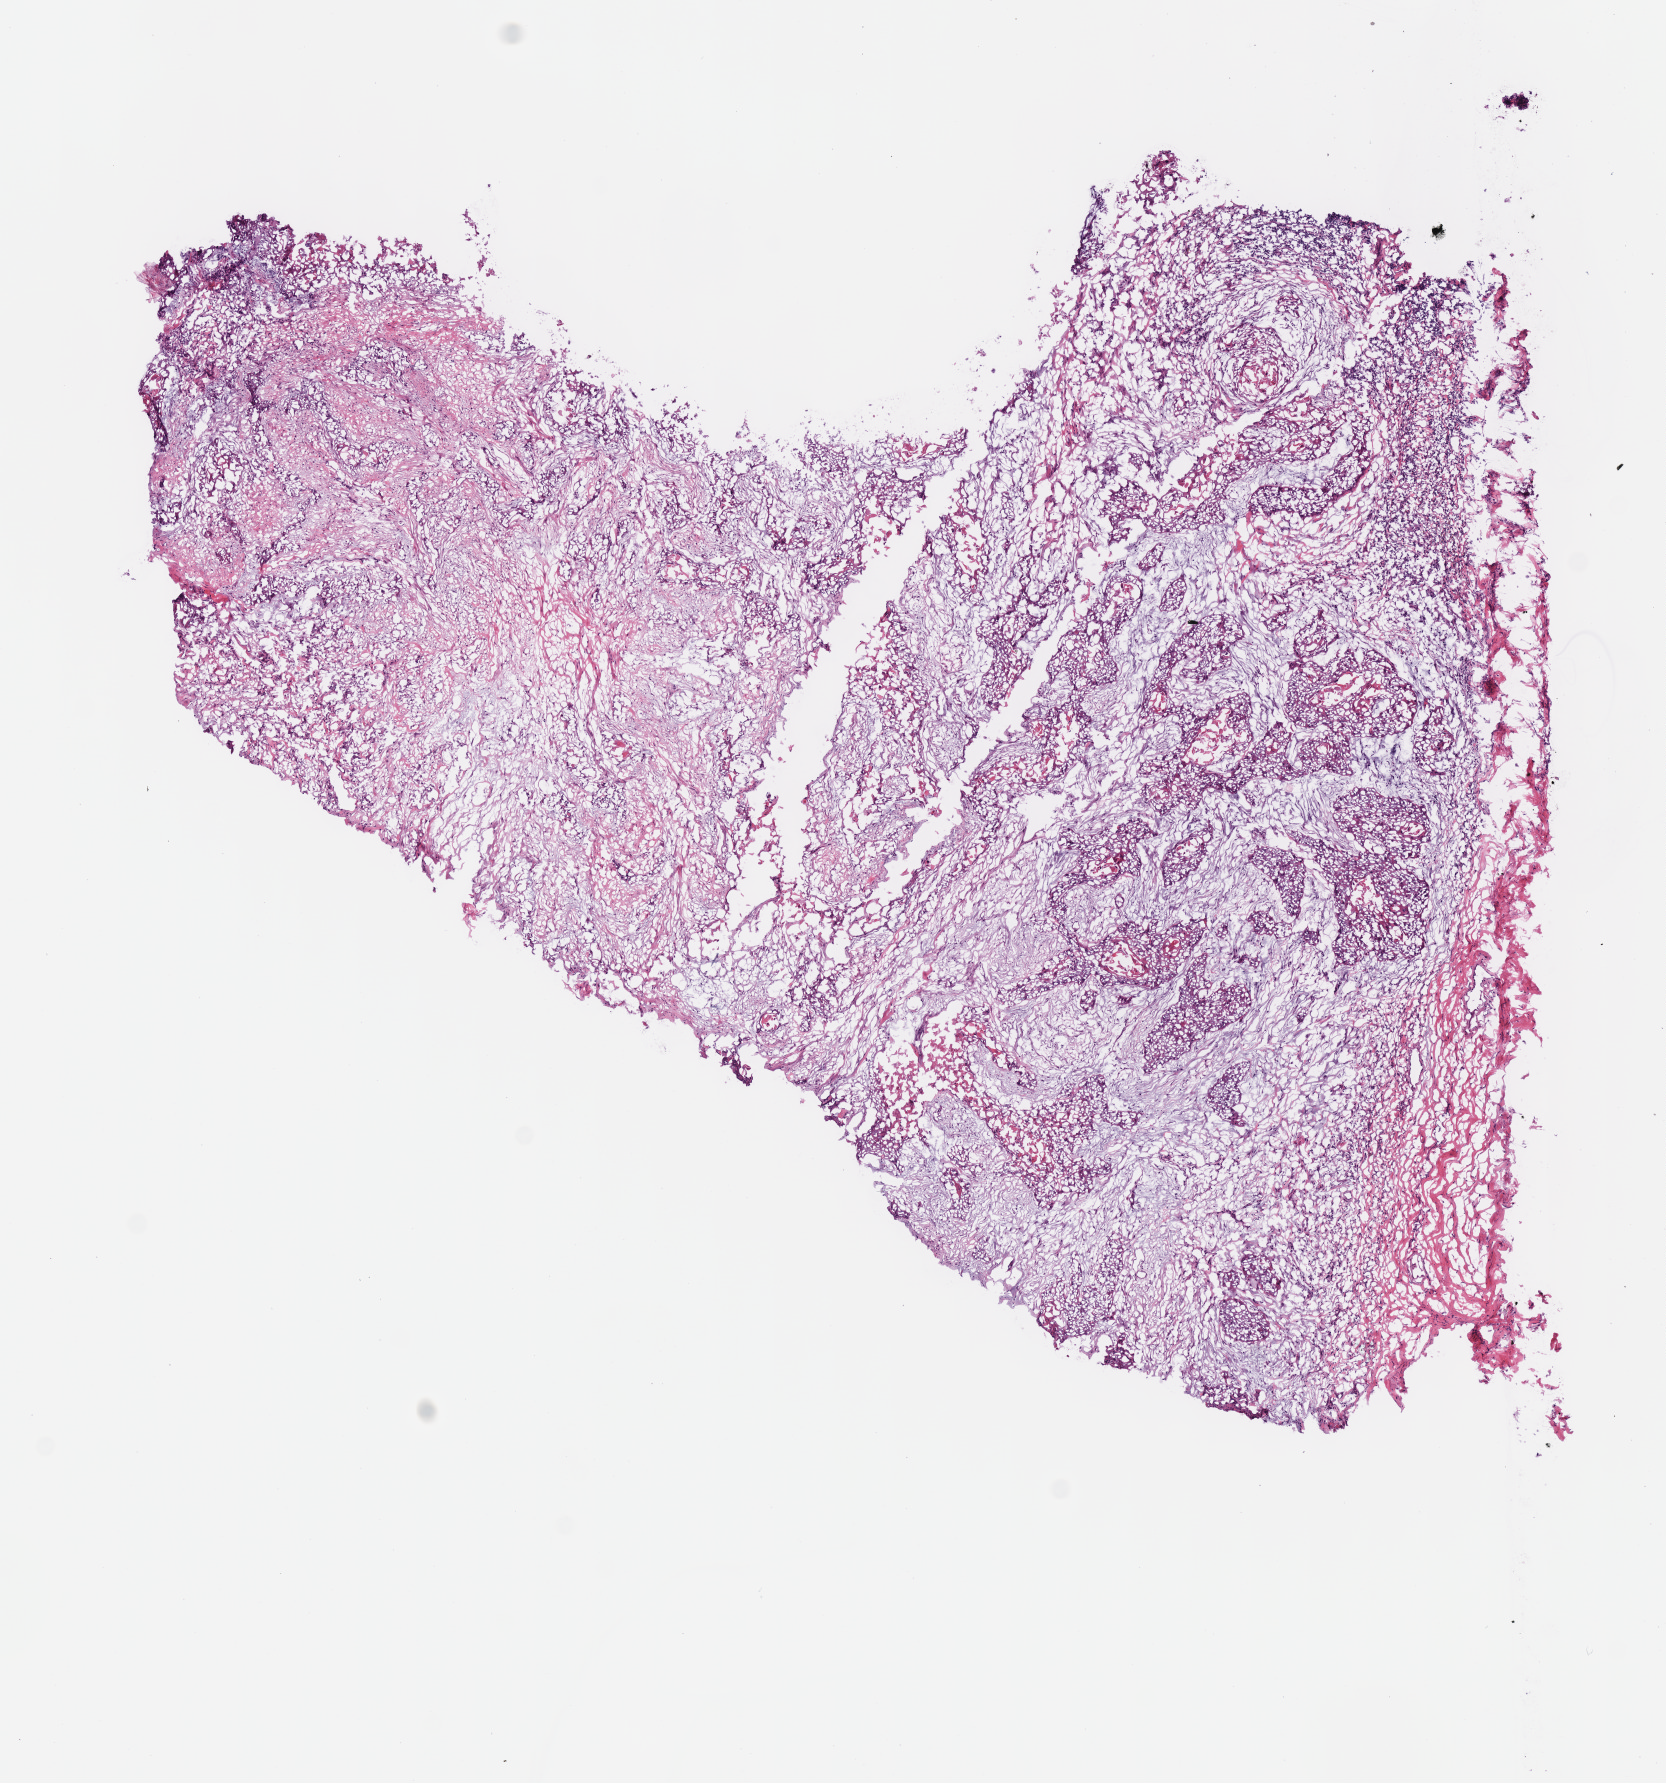
Digitized H&E tissue section (whole slide) — whole scanned area (about 6.6 x 7.0 mm, from a 40x scan) shown as a low-resolution overview; frozen section from the bottom of the tissue portion; head and neck, primary tumour sample. Male patient; age at initial diagnosis 76 years. Slide review estimates, as recorded: tumour cells 100%, tumour nuclei 75%.
Diagnosis: Squamous cell carcinoma, NOS (larynx, NOS).